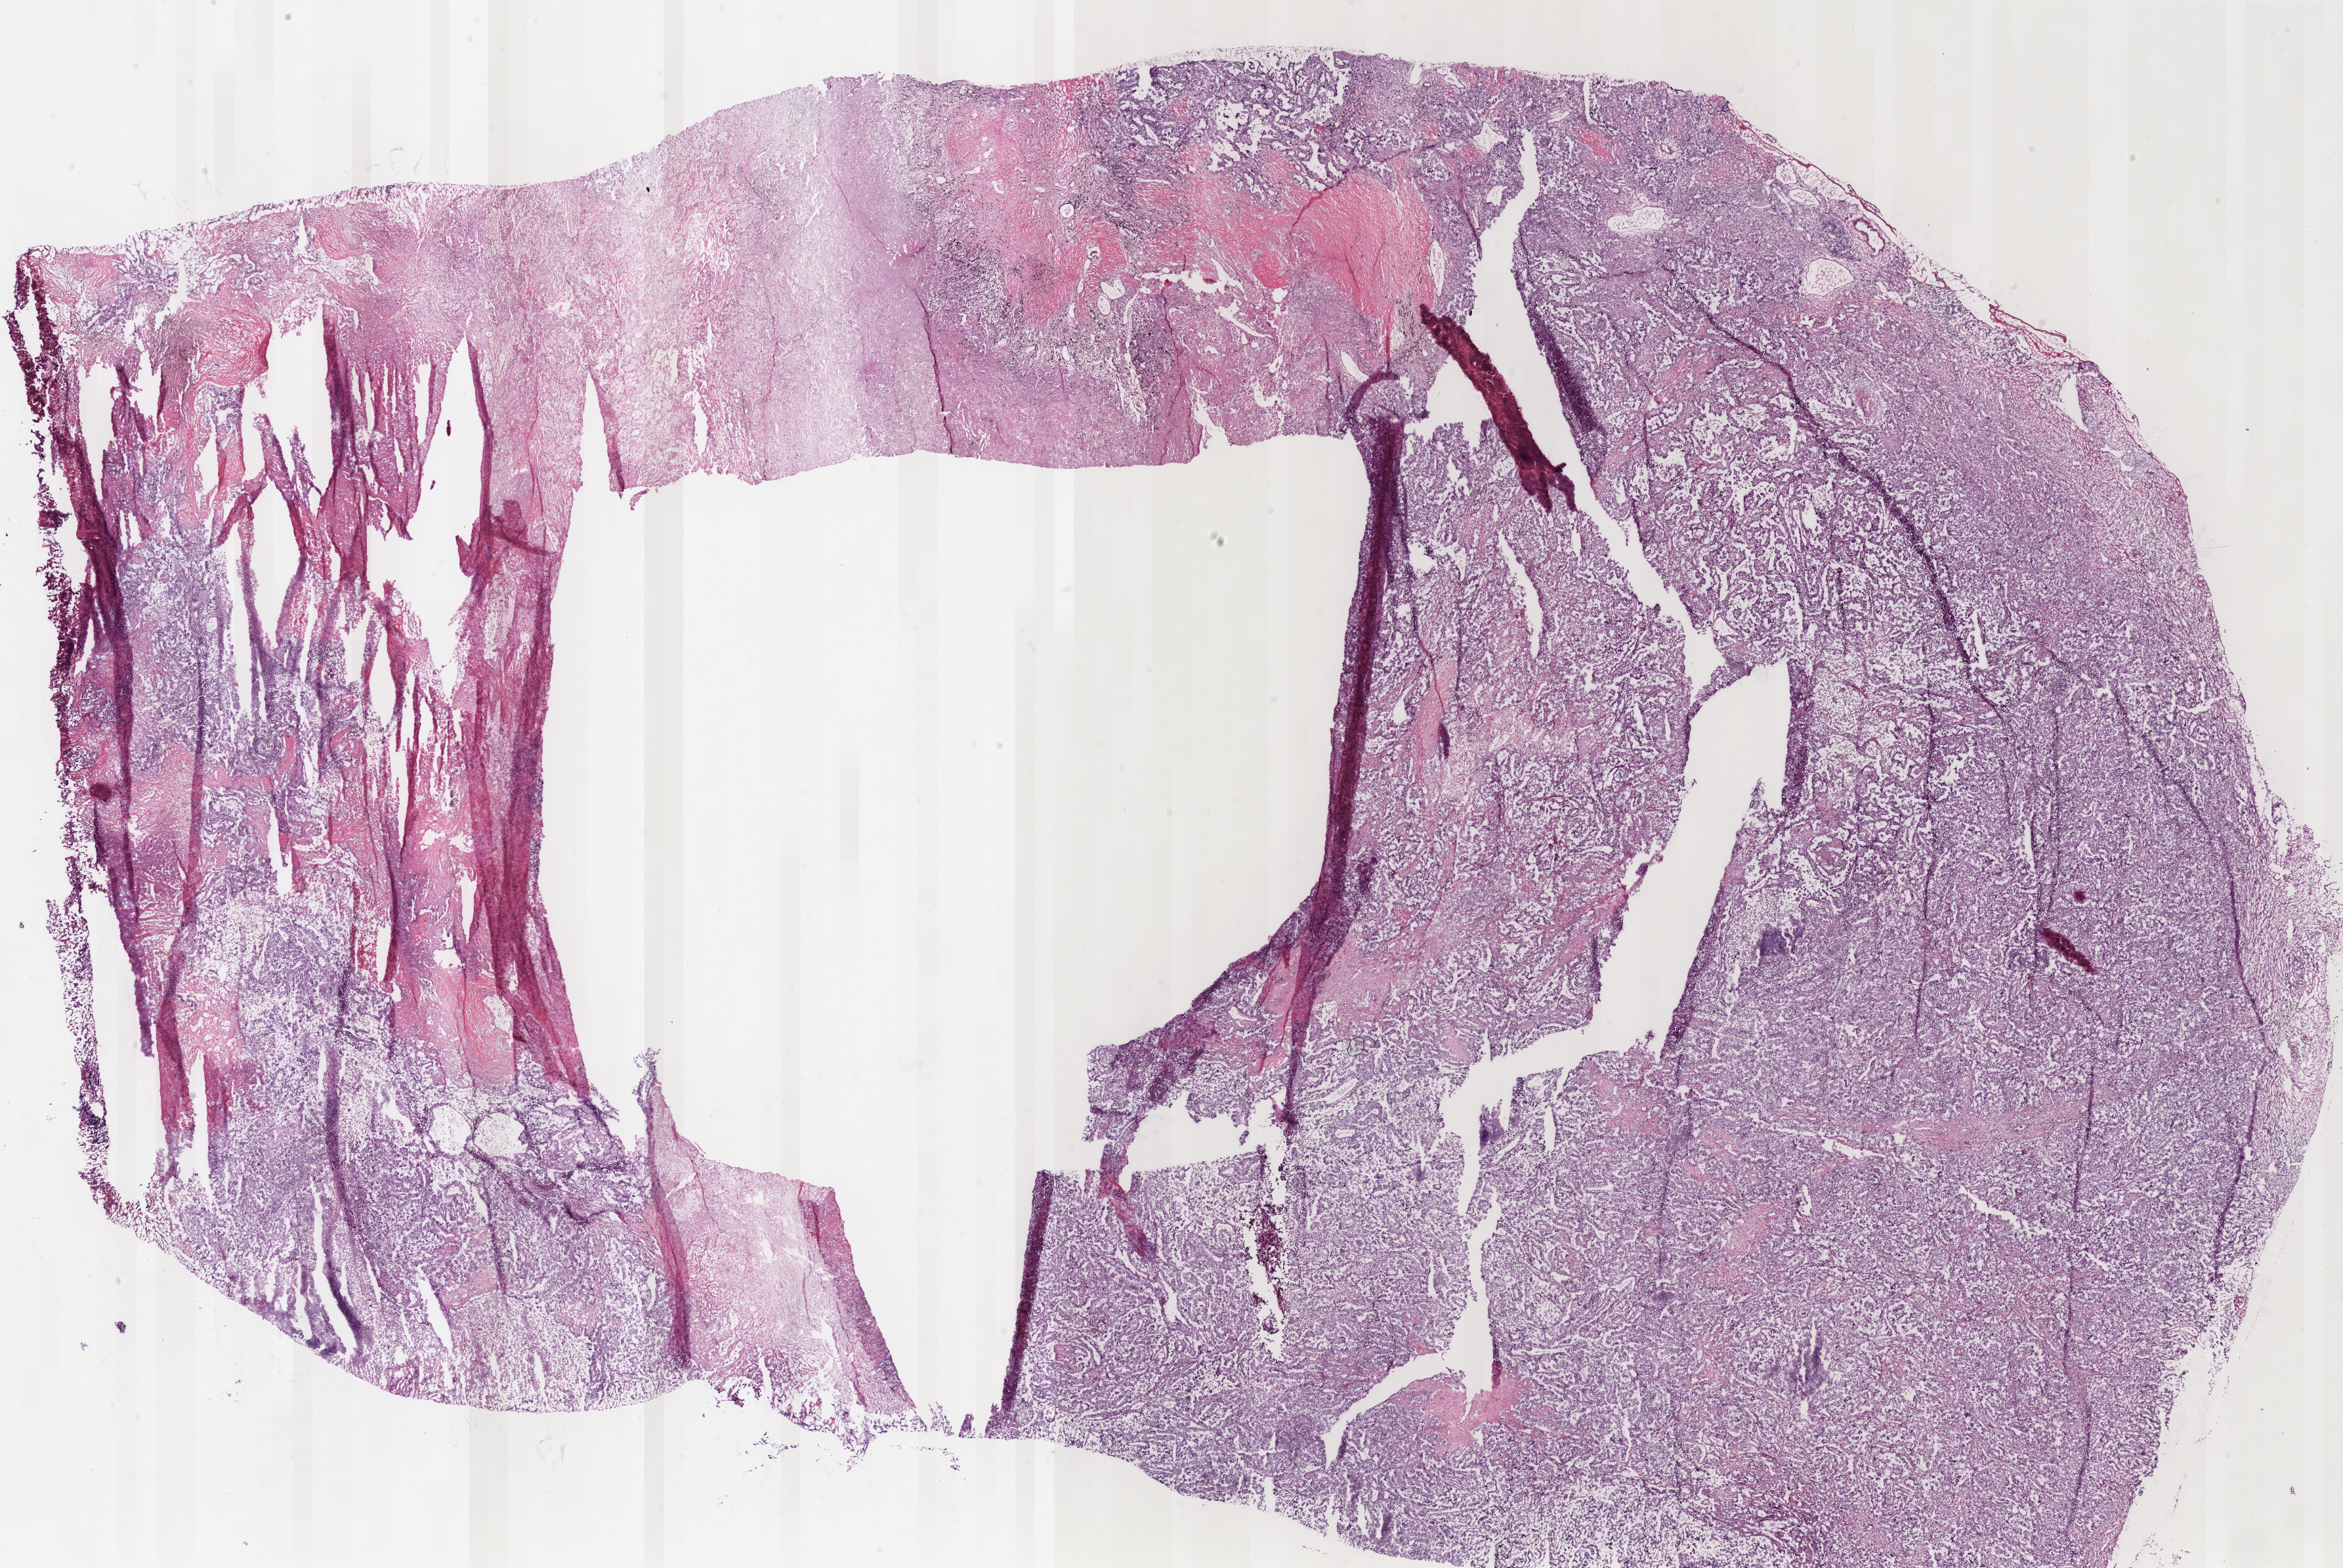
Hematoxylin and eosin (H&E) stained whole-slide image — low-resolution overview of the scanned area, about 28.1 x 18.8 mm (acquisition: 40x scan); frozen section from the bottom of the tissue portion; lung, primary tumour sample. Patient: male, age at initial diagnosis 61 years. Pathologist review of this section (percent, as recorded): tumour cells 80%, tumour nuclei 65%, normal cells 0%, stromal cells 2%, necrosis 18%. Infiltration values recorded for this section: lymphocyte infiltration 17%, monocyte infiltration 0%, neutrophil infiltration 10%.
* AJCC pathologic stage: IB
* diagnosis: Bronchiolo-alveolar carcinoma, non-mucinous (upper lobe, lung)
* TNM: T2 N0 M0